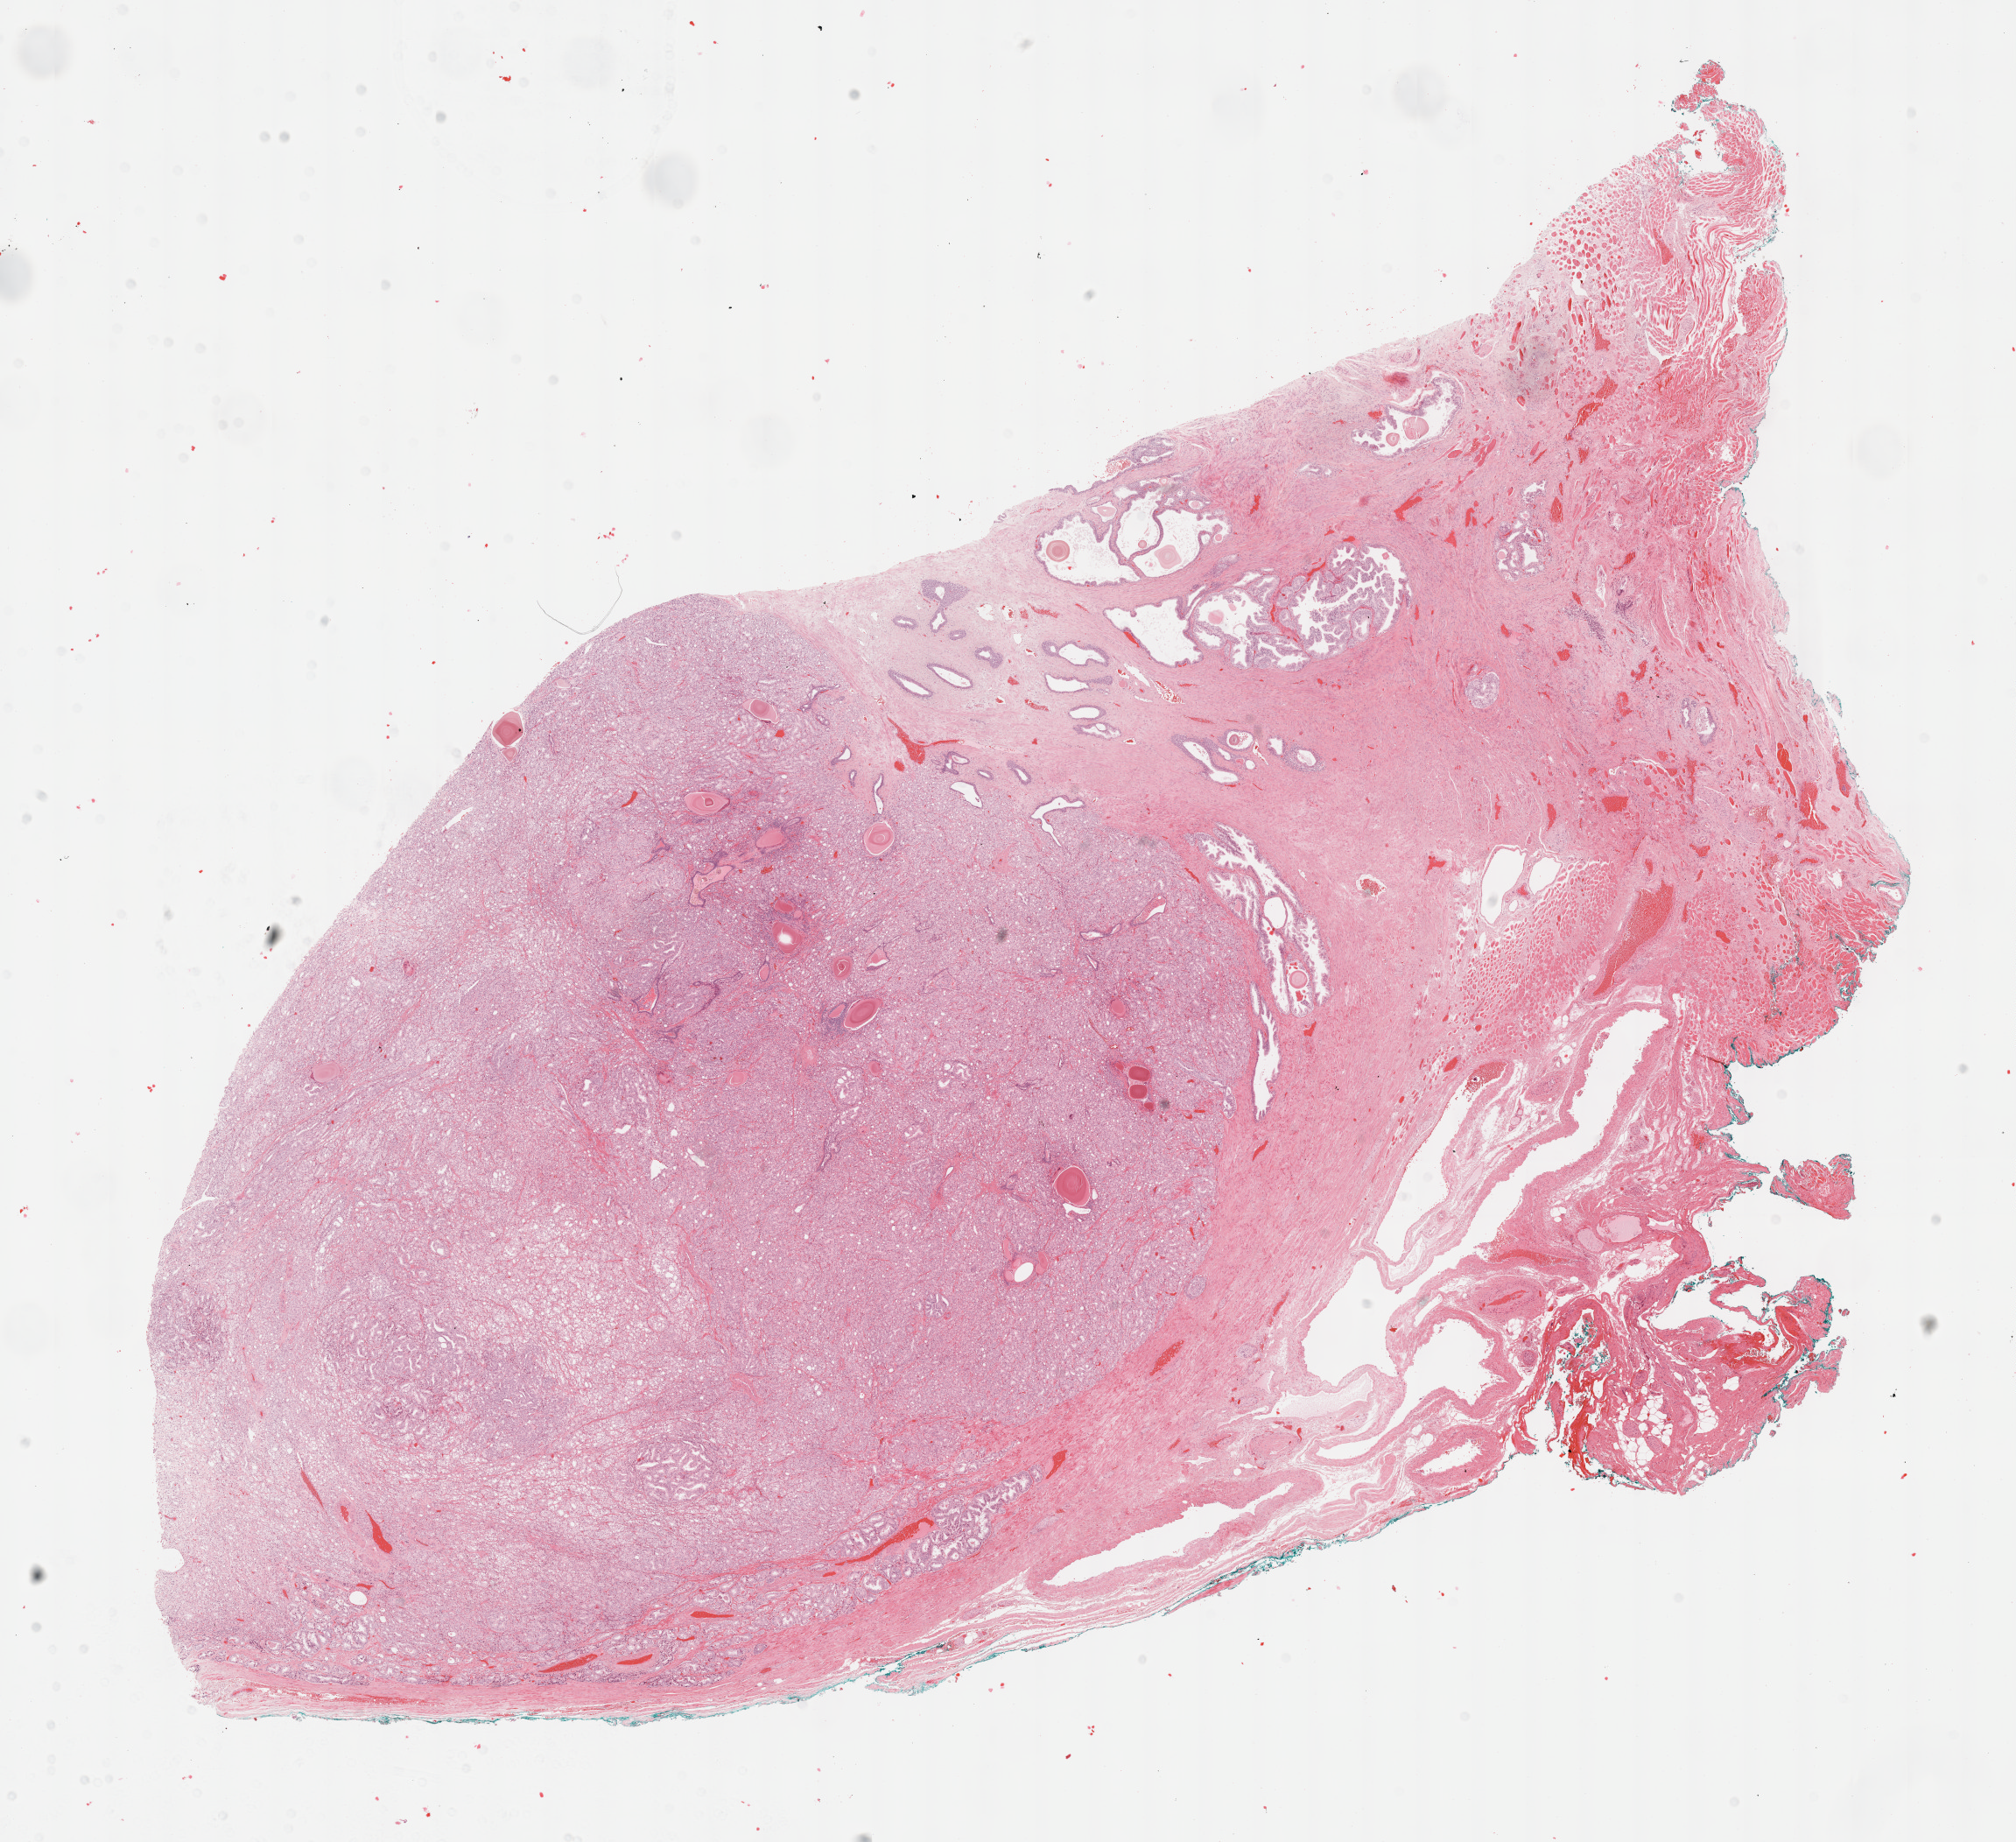
H&E whole-slide image — shown as a low-resolution overview of the whole scanned area (about 18.6 x 17.0 mm), formalin-fixed paraffin-embedded (FFPE) diagnostic section, sample: primary tumour, prostate. Male, age 72 years at initial diagnosis.
Histologic diagnosis: Adenocarcinoma, NOS (prostate gland).